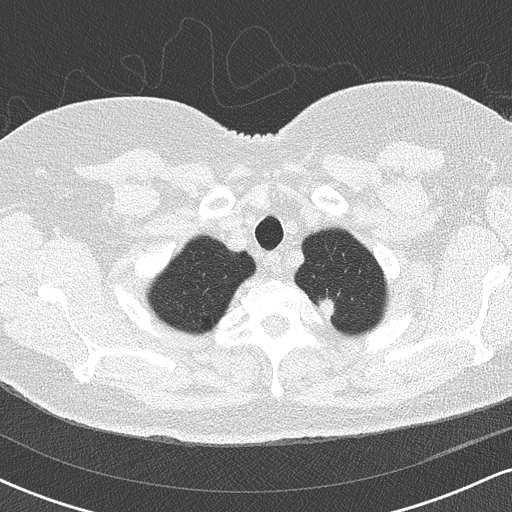
Low-dose screening chest CT, axial slice; third screening round (two years after baseline); lung window (W 1500 / L -600 HU); 2 mm slice thickness; lung (sharp) reconstruction kernel (B50f); 120 kVp; 512 × 512 image matrix, field of view 320 × 320 mm. Female participant, aged 60 years at enrolment. Former smoker at enrolment.
Expert-annotated lung lesion, bounding box [x1, y1, x2, y2] px = [299, 286, 349, 329]. Reader record for this screening exam (exam-level; its link to the box is not recorded): non-calcified nodule or mass ≥4 mm, left upper lobe, 10 × 10 mm, soft tissue attenuation, pre-existing on the prior screen: yes. Official screen result: positive, no significant change: stable abnormalities potentially related to lung cancer, unchanged since the prior screening exam. Later outcome: lung cancer diagnosed 94 days after this screen — non-small cell carcinoma, left upper lobe, poorly differentiated (G3), stage IB (AJCC 6th edition), 16 mm at pathology.